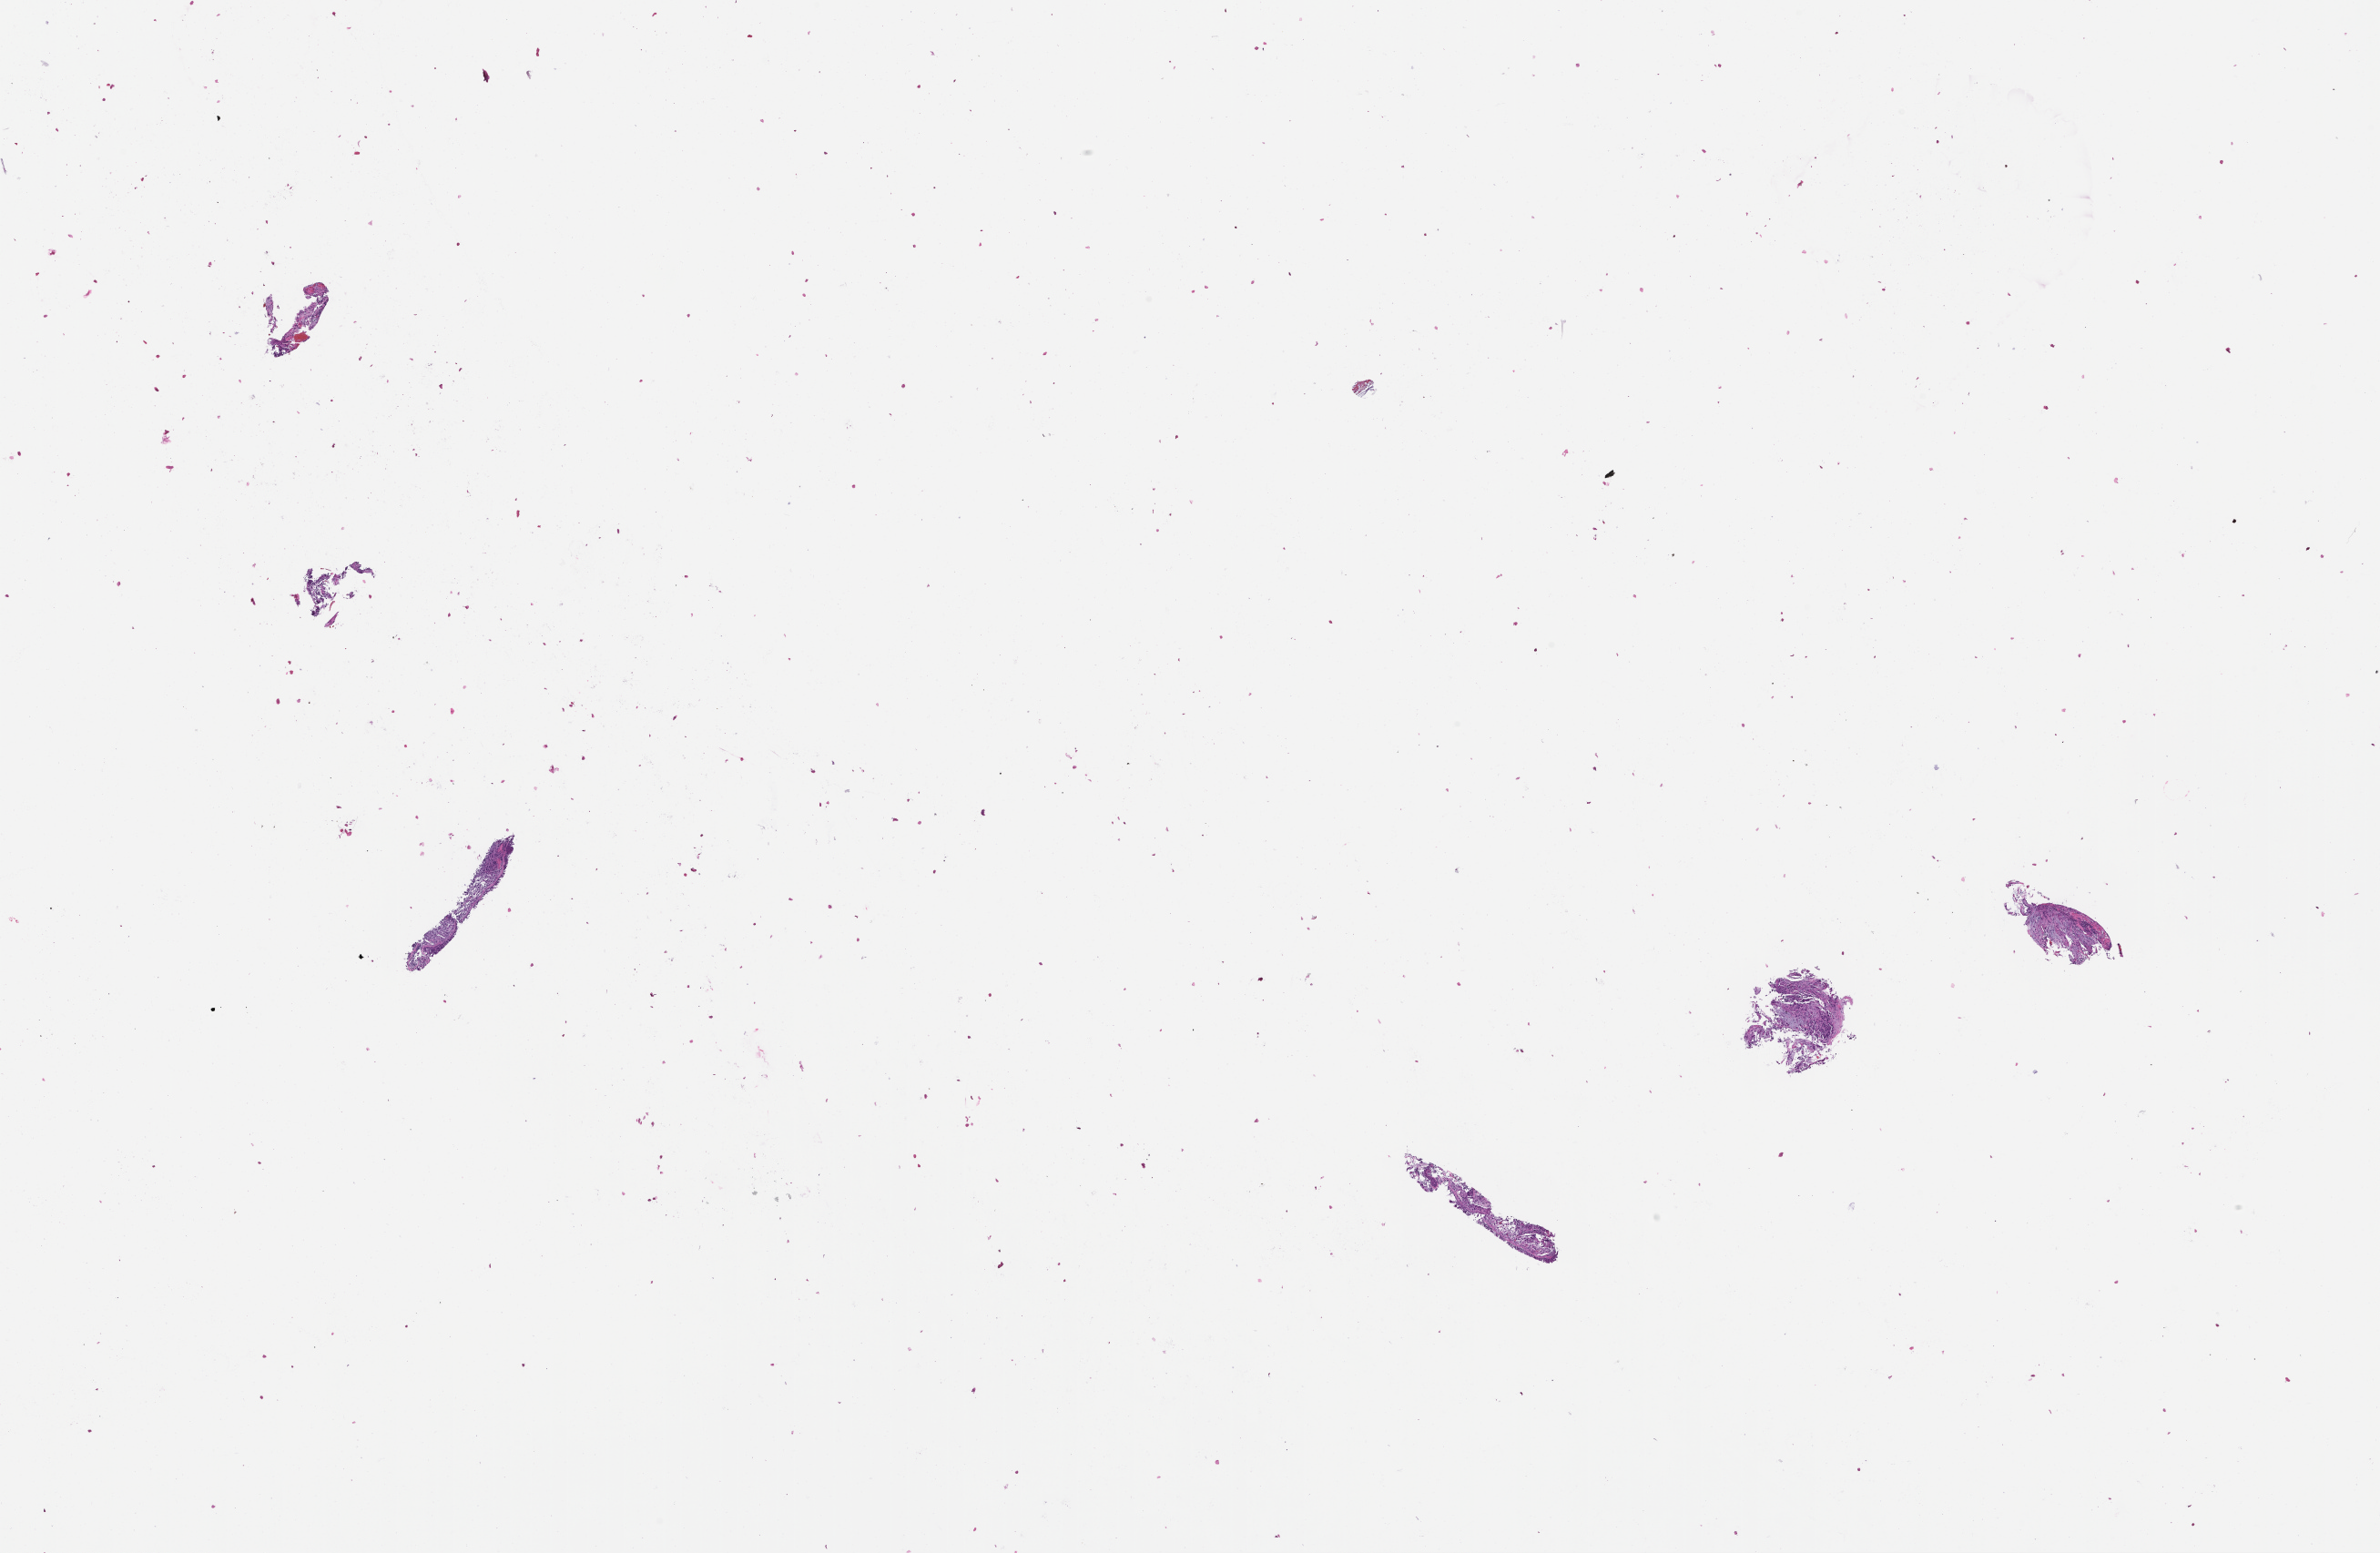
Whole-slide image, hematoxylin and eosin (H&E) stain, whole scanned area (about 21.1 x 13.8 mm) shown as a low-resolution overview, formalin-fixed, paraffin-embedded (FFPE) tissue, tissue site: lung. Patient sex: female.
- this section: primary tumor
- diagnosis: Non-Small Cell Lung Carcinoma